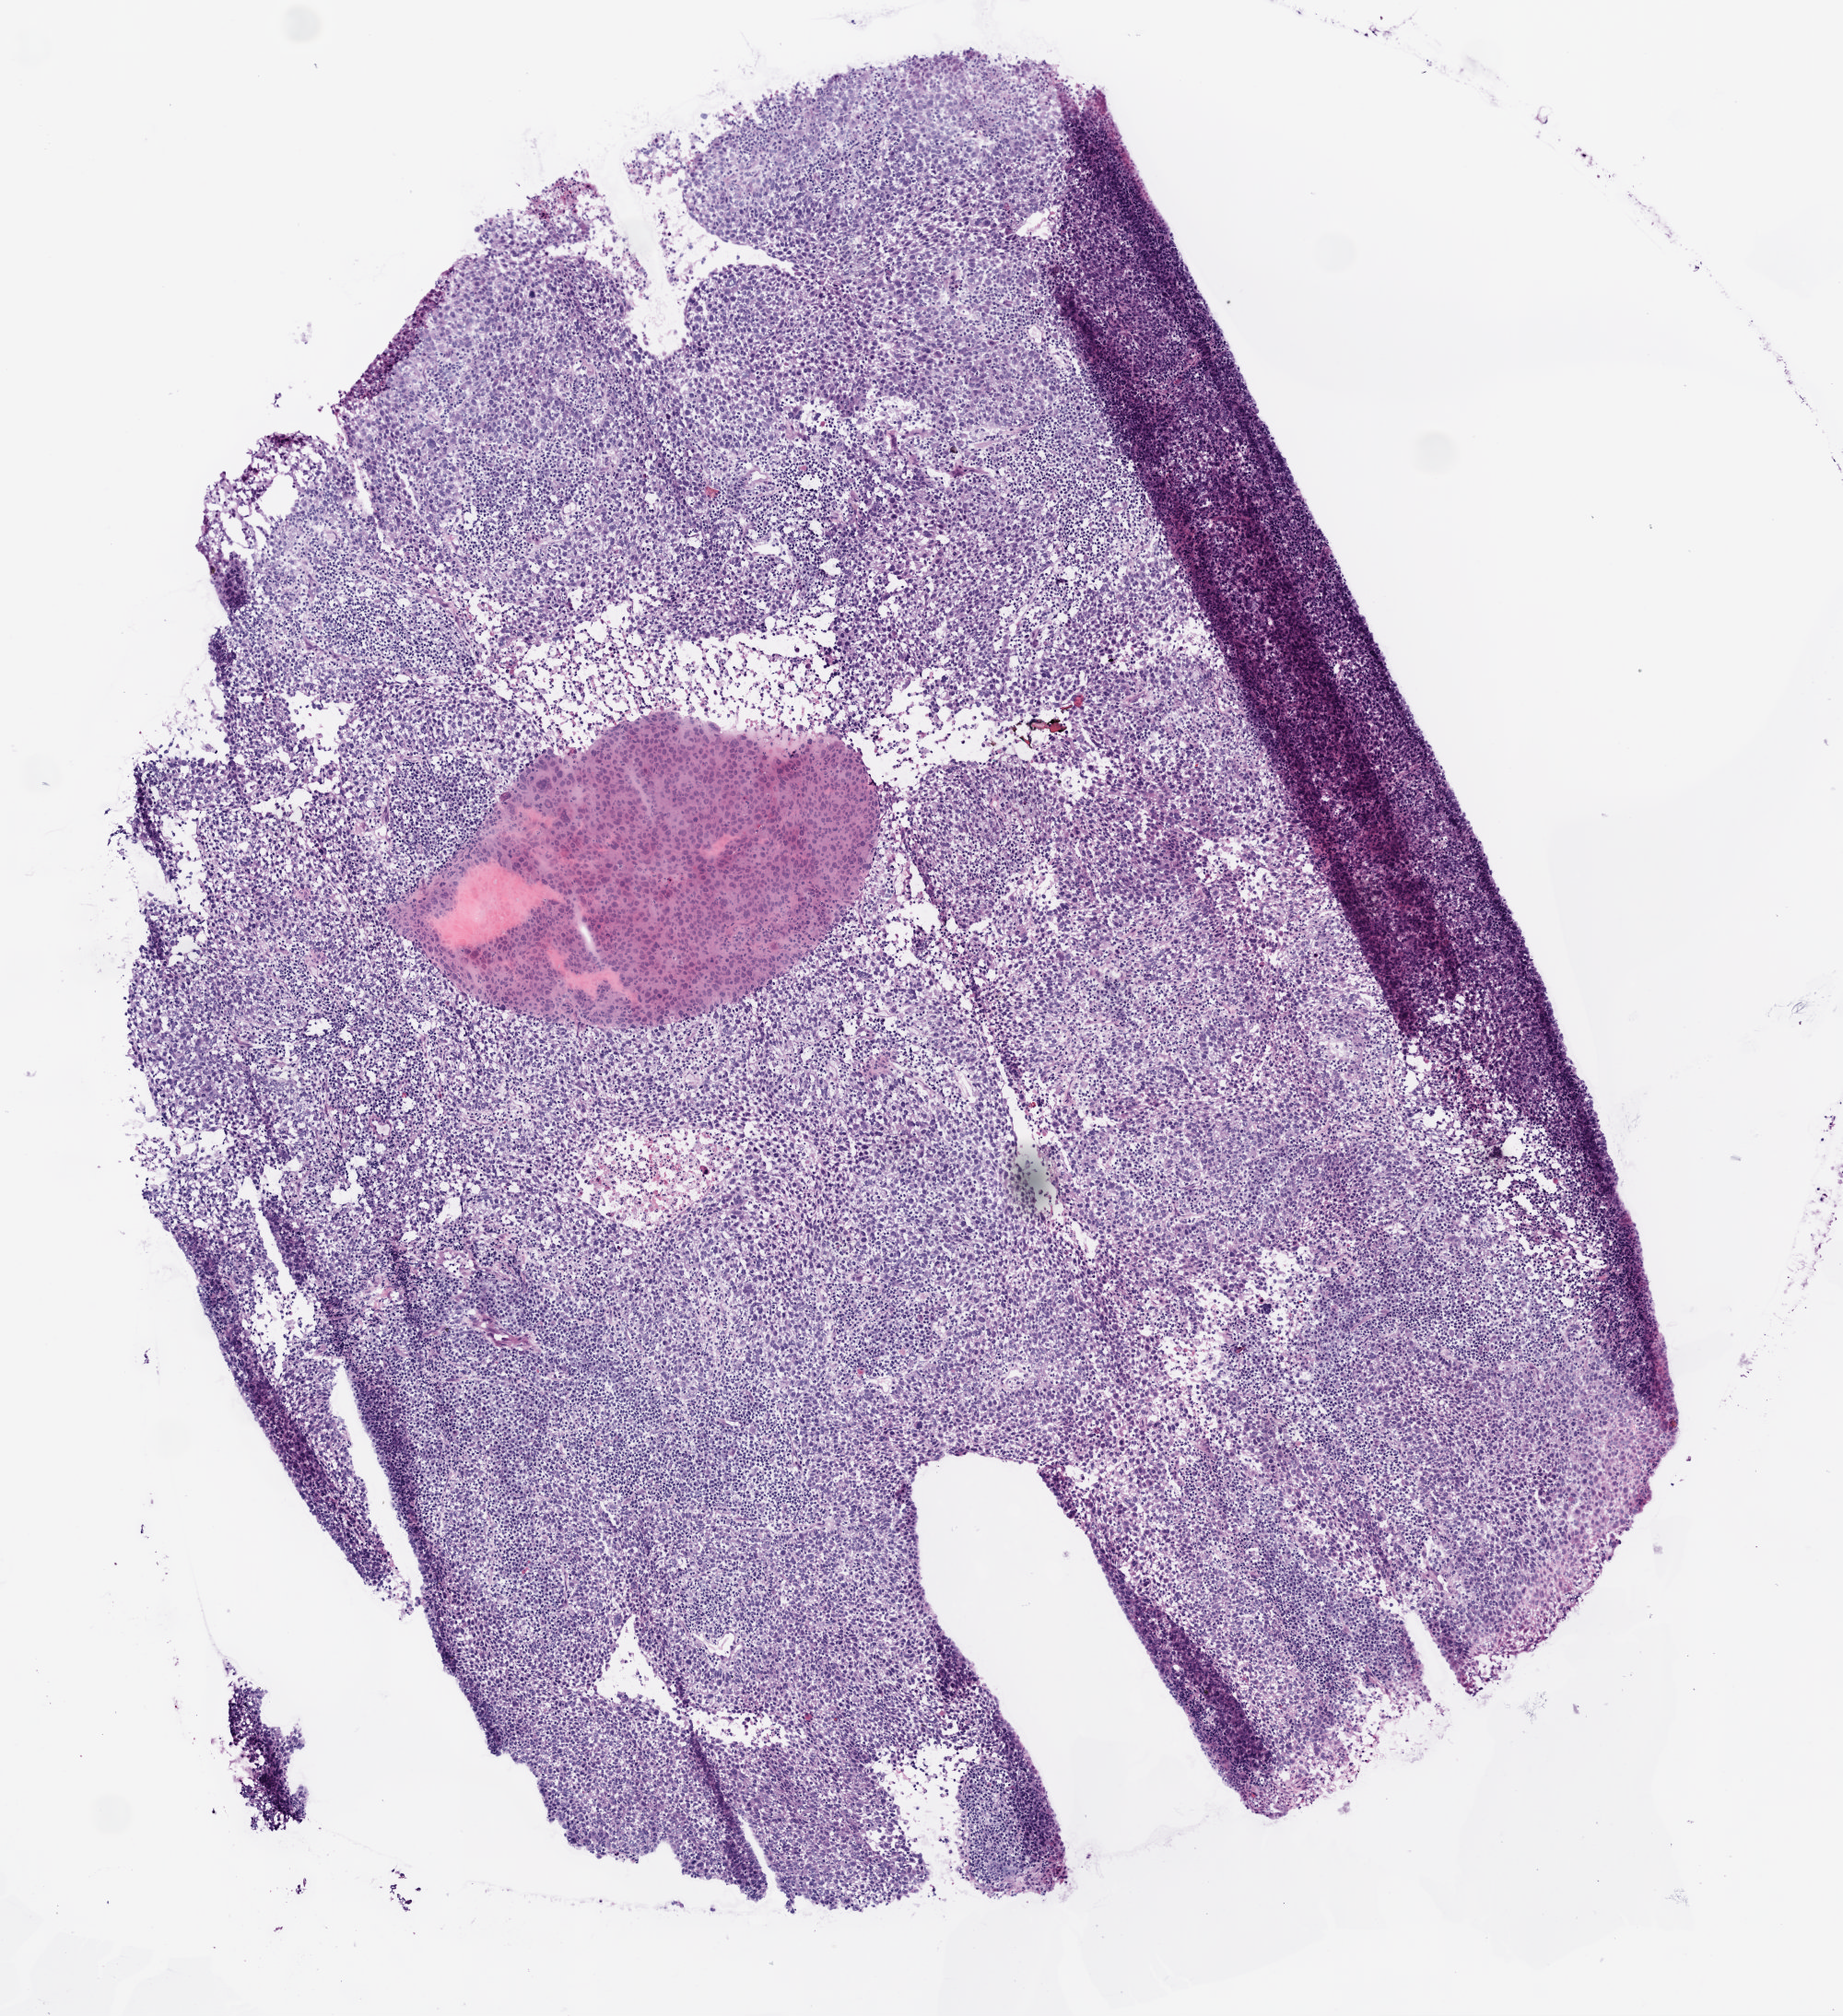
Whole-slide histology image, H&E-stained — a low-resolution overview of the entire scanned area, about 4.0 x 4.4 mm. Frozen section from the bottom of the tissue portion. Sample: primary tumour, lung. Male patient; age at initial diagnosis 83 years. Composition of this section per pathologist review: tumour cells 88%, tumour nuclei 70%, normal cells 0%, stromal cells 7%, necrosis 5%. Infiltration values recorded for this section: lymphocyte infiltration 25%.
• pathologic diagnosis: Squamous cell carcinoma, NOS (upper lobe, lung)
• AJCC pathologic stage: IIB